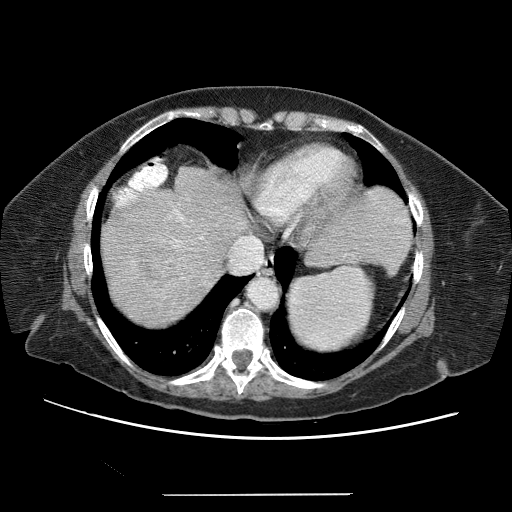
Contrast-enhanced abdominal CT (liver protocol), one axial slice. Position 53 of 65 along the scan axis. Reconstruction kernel STANDARD. 120 kVp. Soft-tissue window (W 400 / L 40 HU). 2.5 mm slice thickness. 512 × 512 image matrix, field of view 380 × 380 mm. From the clinical record (not read from this slice): diagnosis: hepatocellular carcinoma (patient treated with transarterial chemoembolisation; whether this scan precedes or follows treatment is not stated here); TNM stage (as recorded): Stage-IIIB; Child-Pugh class: A; tumour differentiation: moderately differentiated; tumour nodularity: uninodular.
Structures marked on this image (semi-automatically segmented with operator editing):
- abdominal aorta: bounding box [x1, y1, x2, y2] px = [250, 279, 280, 310]
- liver parenchyma outside the tumour (the mass and vessels are separate outlines, so this box may not span the whole liver): [102, 166, 244, 318]
- mass: [132, 239, 182, 289]
- liver vessels: [116, 194, 225, 293]